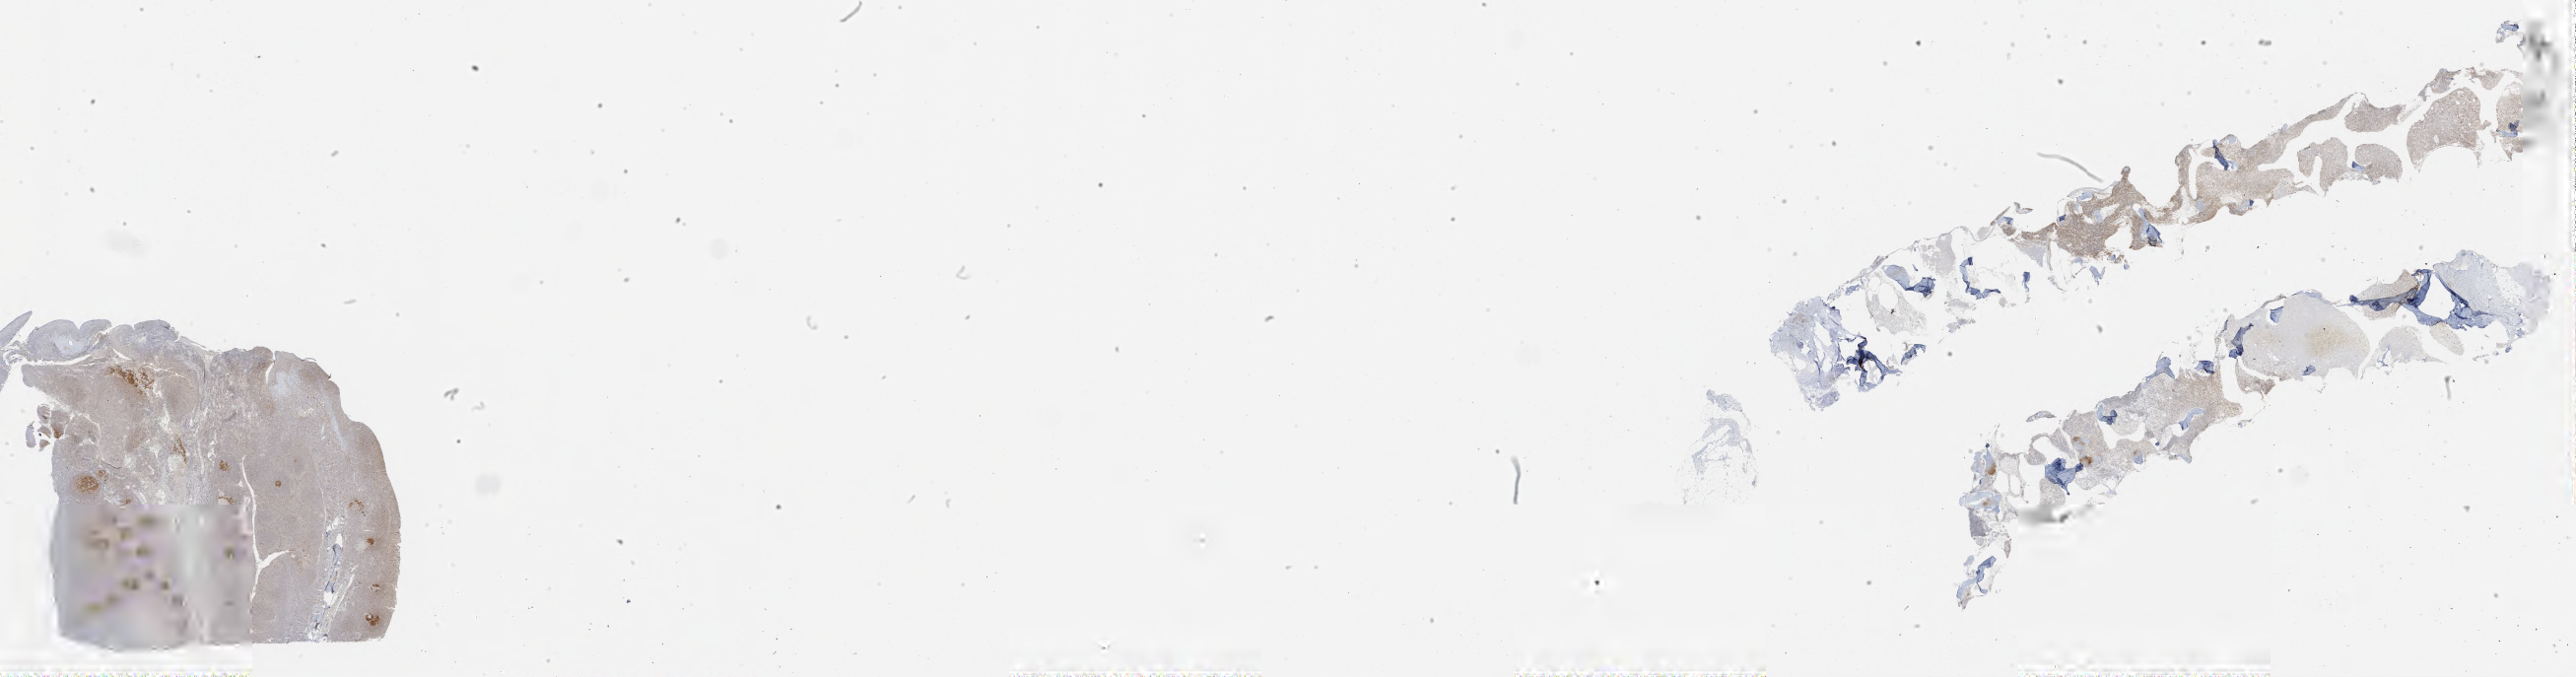
IHC for BCL6, whole-slide image — a low-resolution overview of the entire scanned area, about 42.0 x 11.0 mm, specimen: tumor tissue. Patient female; age 60 years.
Histologic diagnosis: Burkitt lymphoma, NOS.